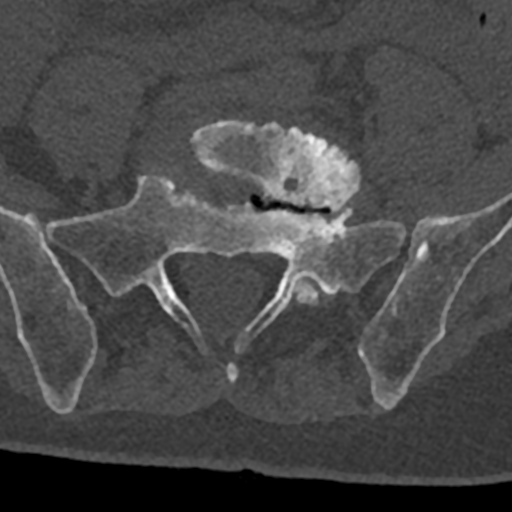
CT including the spine, one axial slice. Slice 163 of 797 in the series (ordered by position). Reconstruction kernel Br40s/3. Bone window (W 1800 / L 400 HU). 512 × 512 image matrix, field of view 160 × 160 mm. Patient: male, 74 years. Case-level facts recorded for this patient, not image findings: primary cancer: renal.
Outlined on this slice (semi-automatically segmented with operator editing):
- L5 vertebra: bounding box [x1, y1, x2, y2] px = [193, 120, 360, 305]